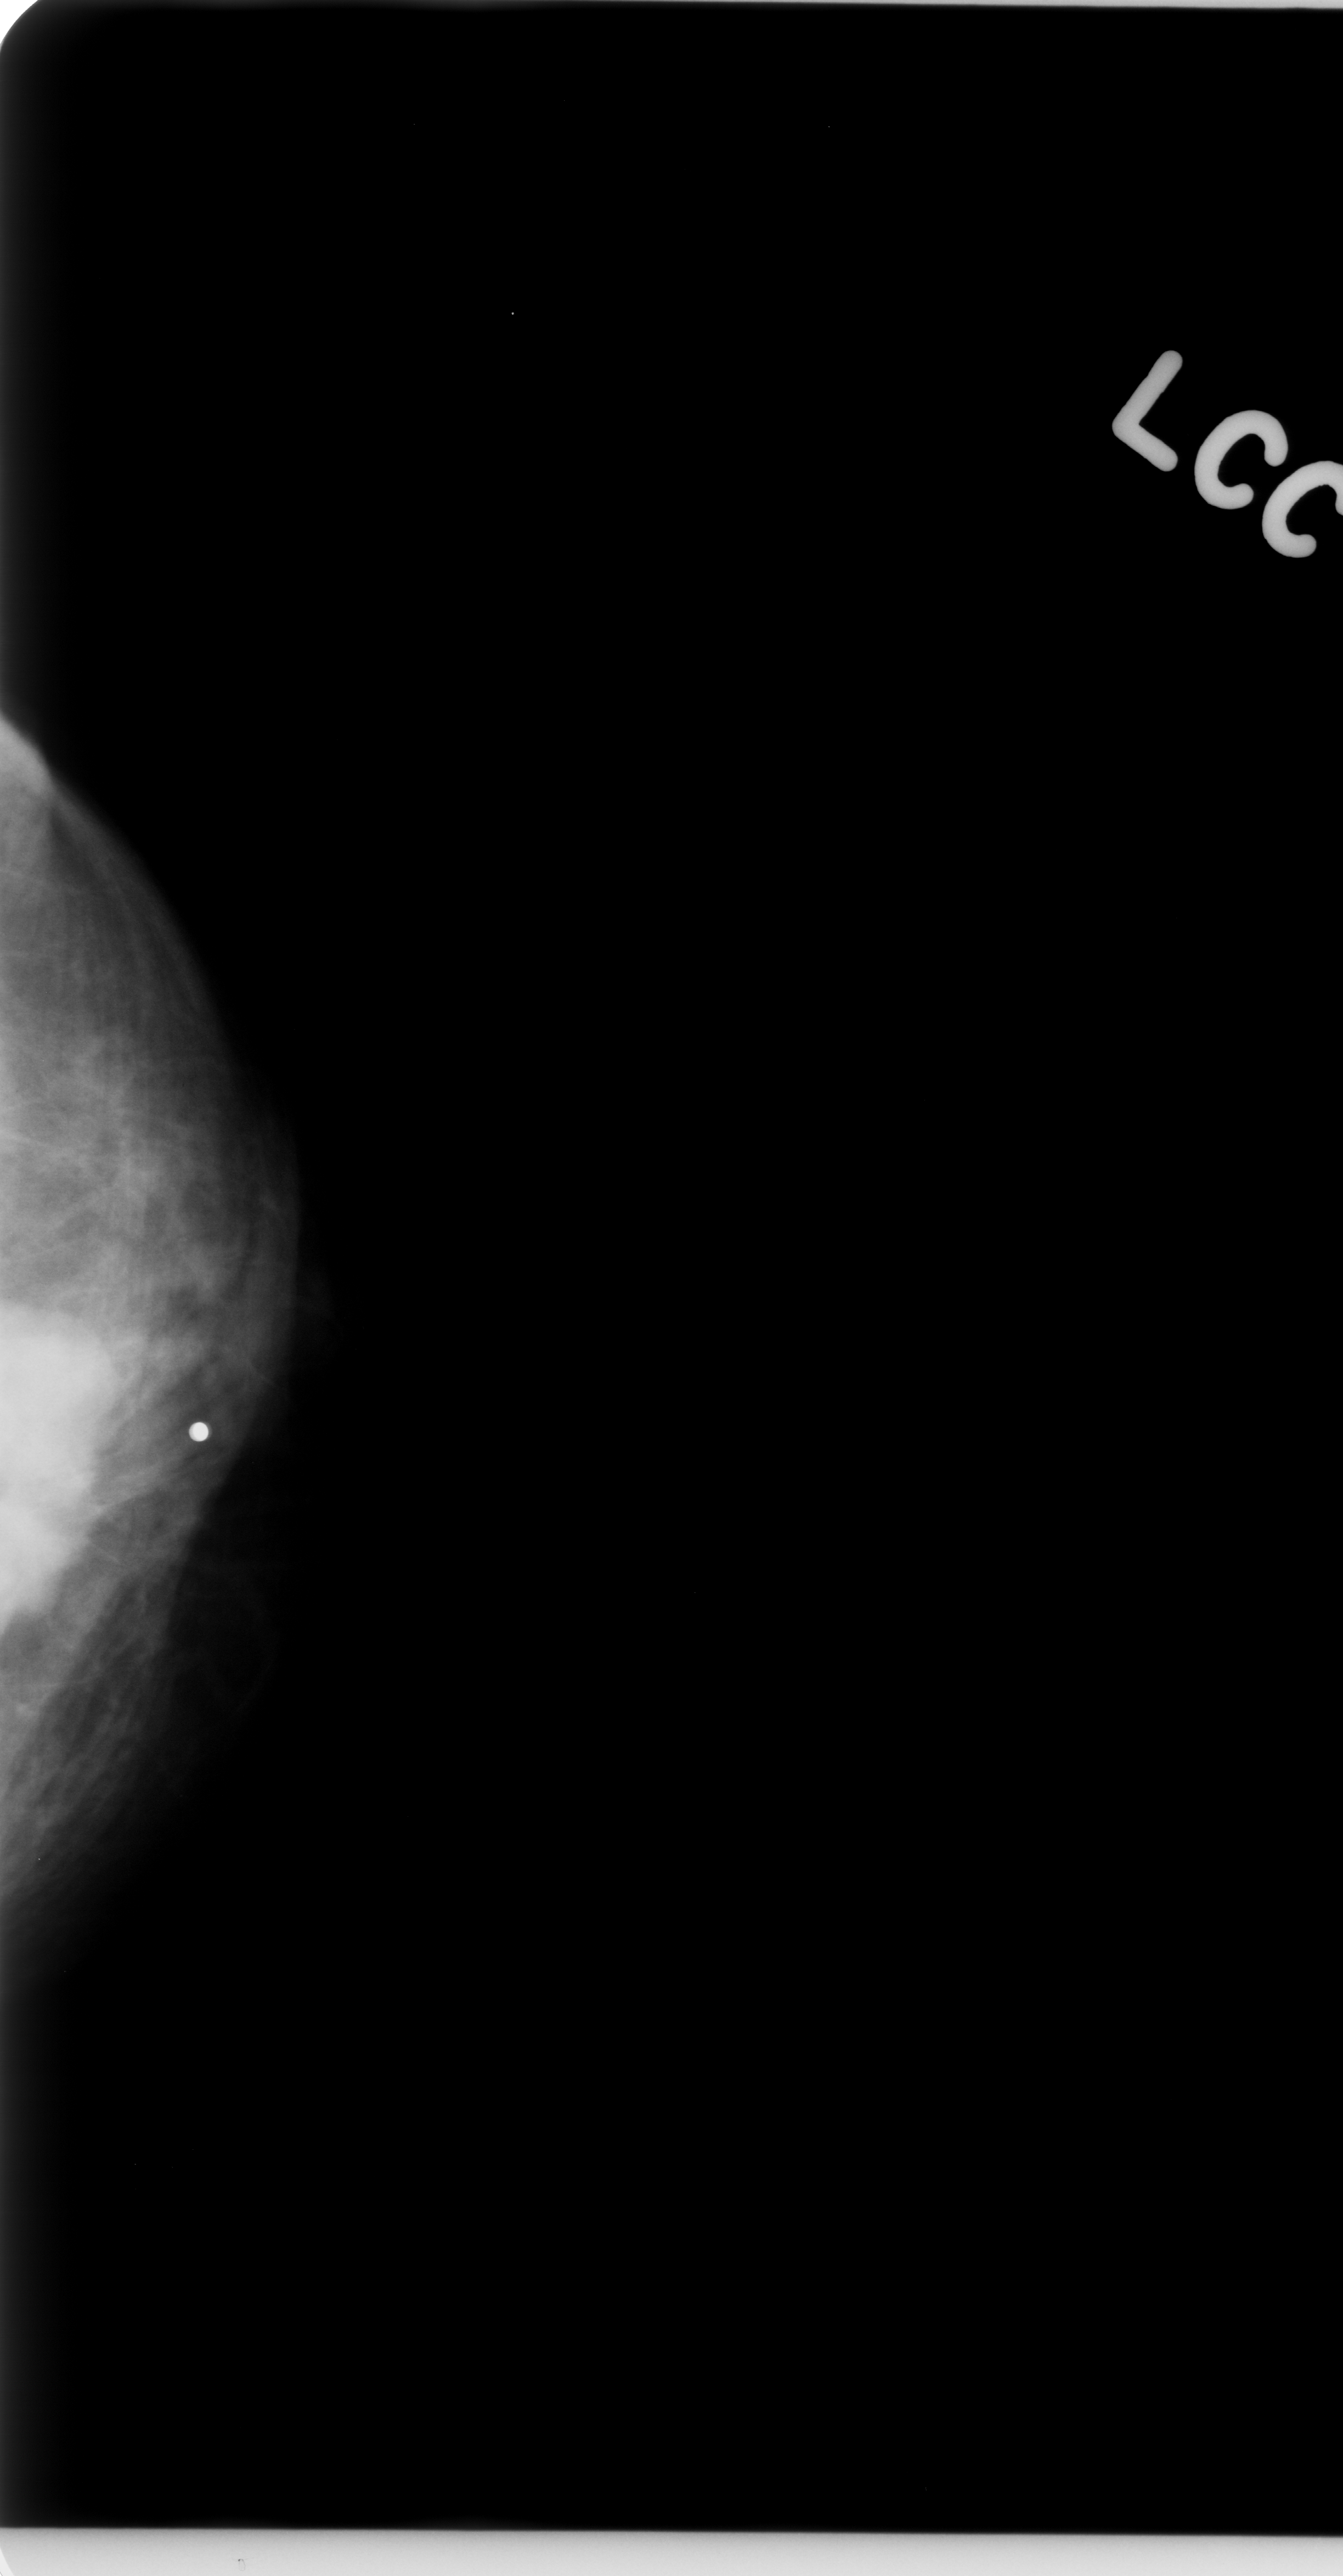
Mammogram (digitized film); left breast; CC view; BI-RADS breast density category 2 (scale 1–4); 1343 × 2576 image matrix.
Expert-marked regions of interest on this film, with their recorded descriptors:
- mass, shape irregular, margins microlobulated; BI-RADS assessment category 5; subtlety rating 5 on a 1 (subtle) to 5 (obvious) scale; pathology (as recorded): malignant: box from (x=13, y=1291) to (x=131, y=1536) px